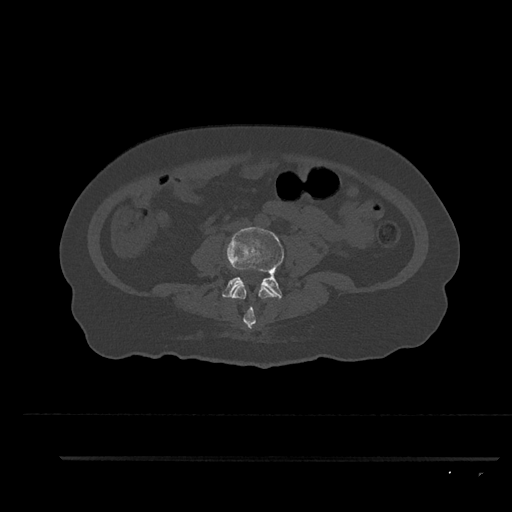
CT including the spine, one axial slice. Slice 46 of 797 in the series (ordered by position). 120 kVp. Bone window (W 1800 / L 400 HU). 512 × 512 image matrix, field of view 408 × 408 mm. Patient: female, 44 years. Case-level facts recorded for this patient, not image findings: primary cancer: renal; vertebrae with lytic lesions (as recorded): L1.
Annotated regions visible in this slice (semi-automatically segmented with operator editing):
- L3 vertebra: bounding box [x1, y1, x2, y2] px = [231, 285, 281, 329]
- L4 vertebra: [222, 227, 284, 299]